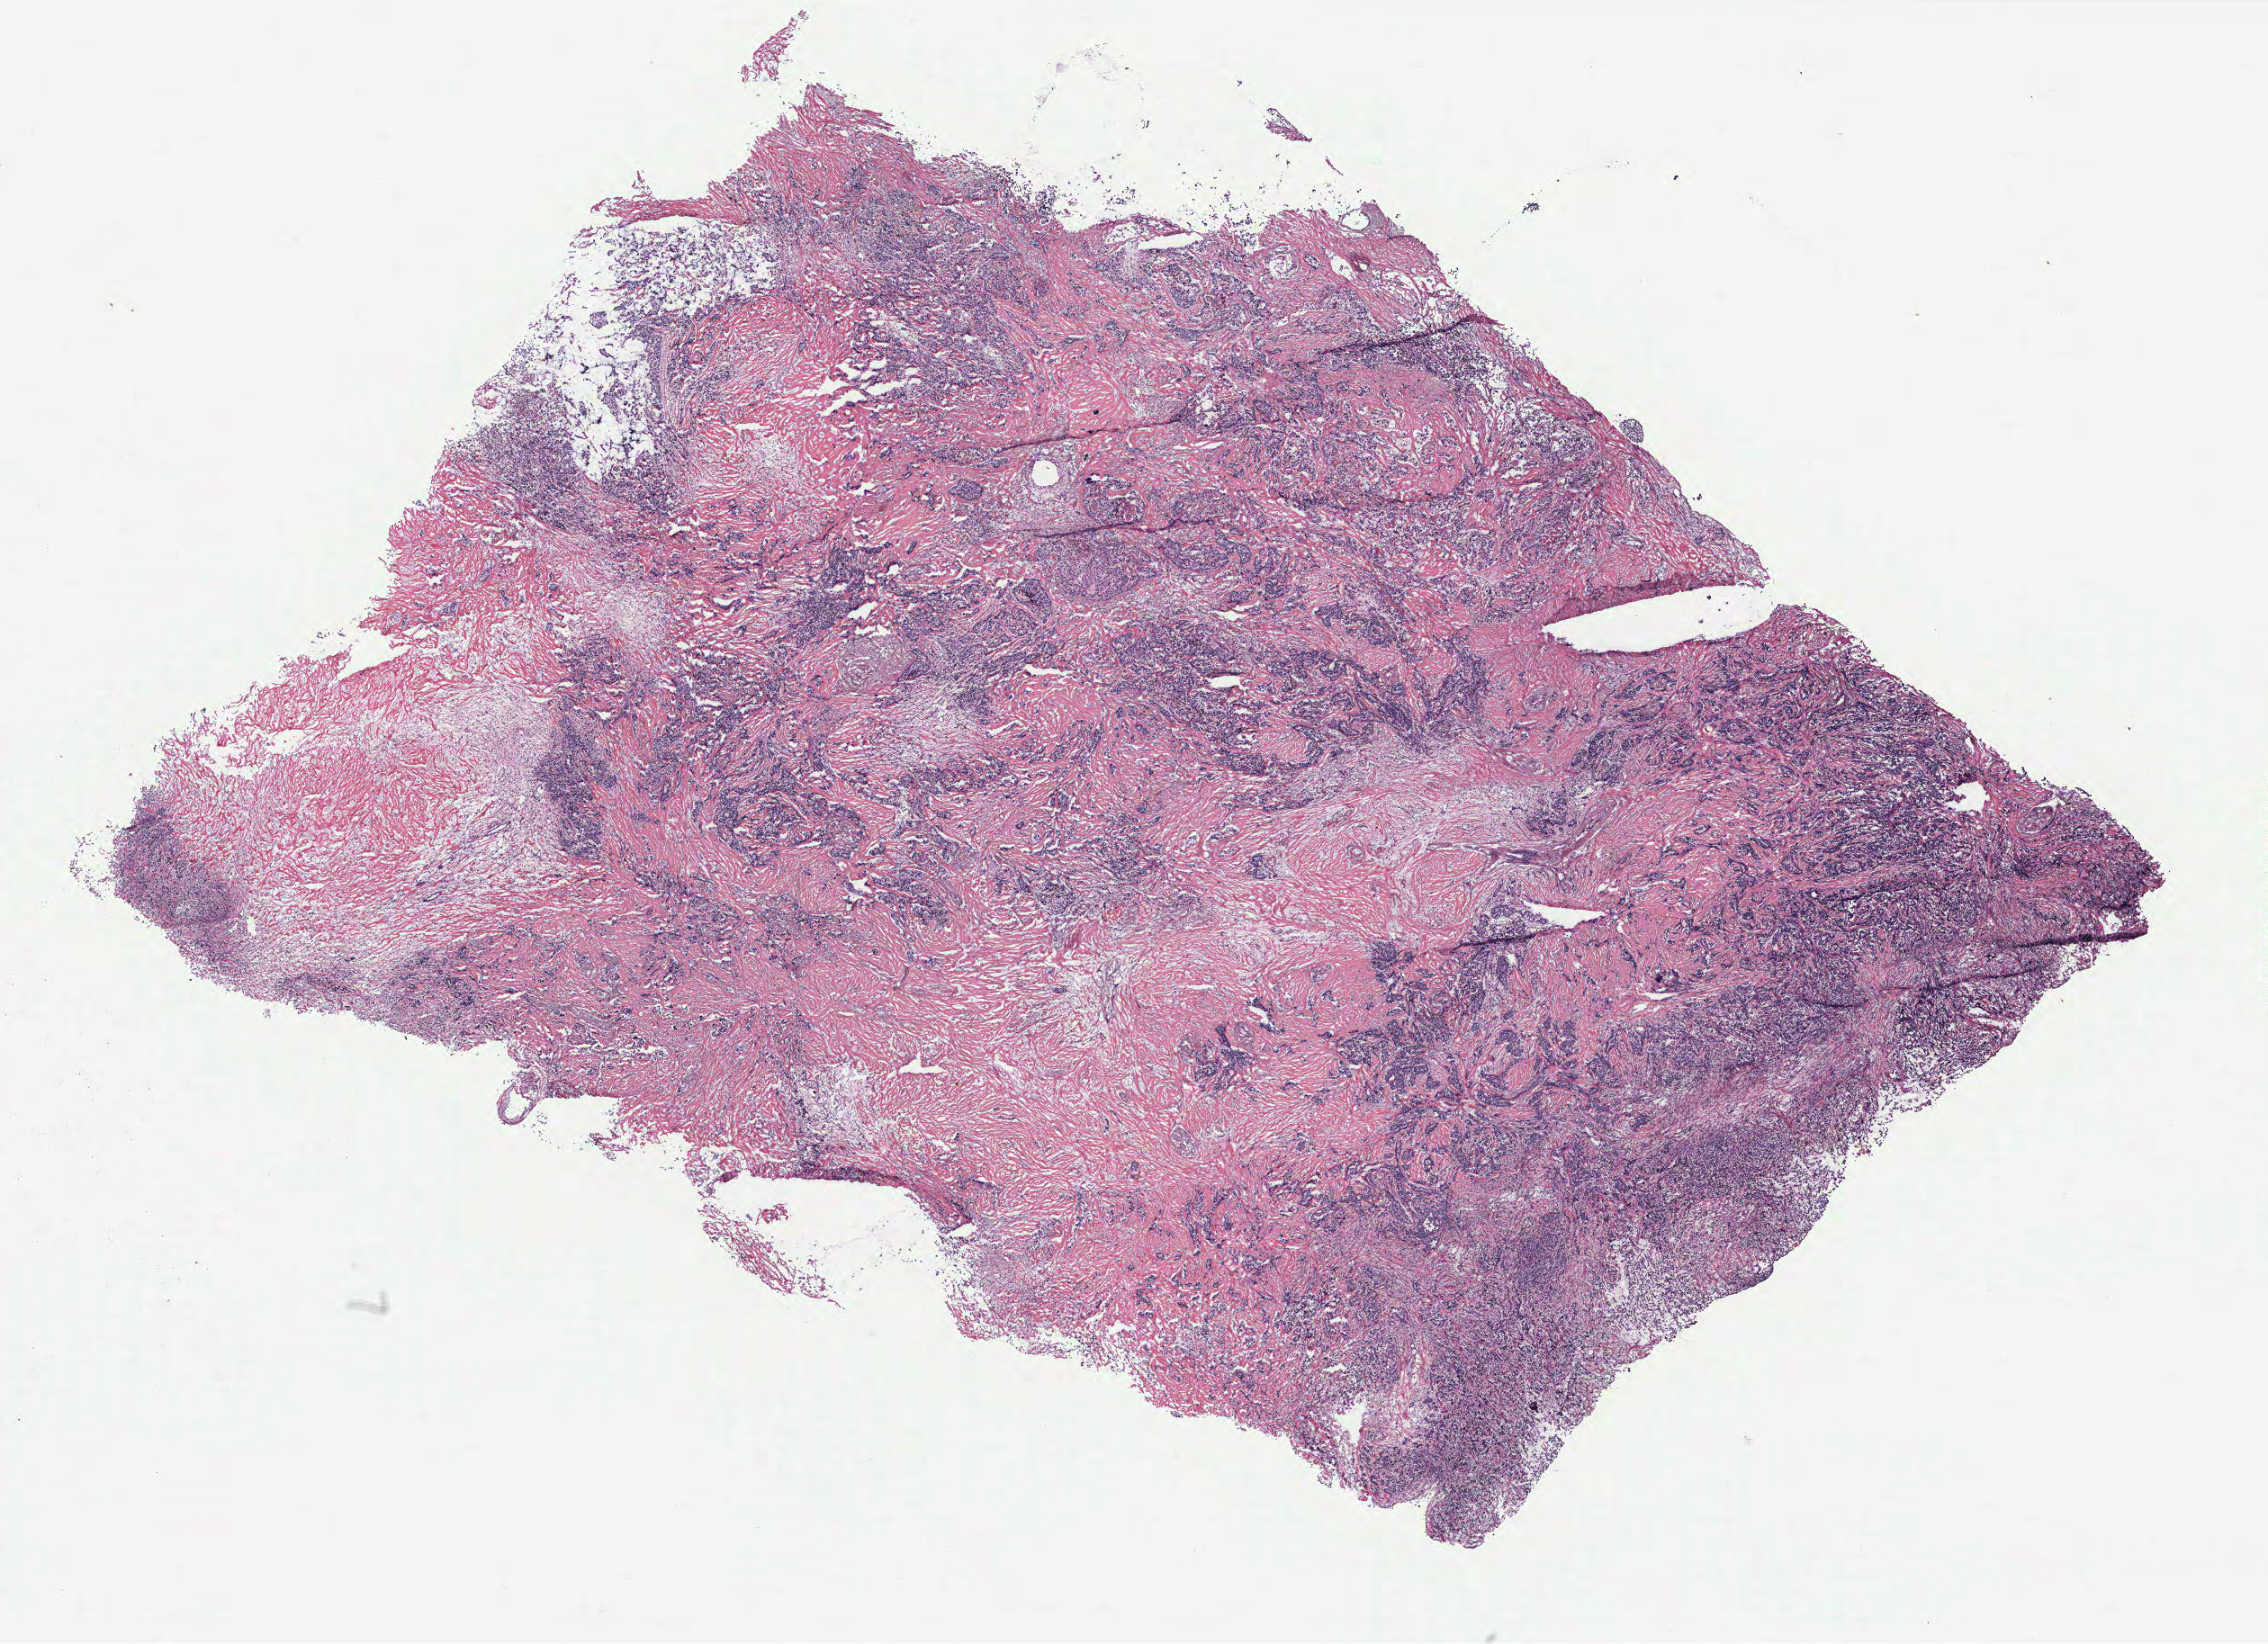
H&E whole-slide image — low-resolution overview of the scanned area, about 20.2 x 14.6 mm (acquisition: 40x scan), breast, tumour tissue. Female, 65 y/o.
* diagnosis: Infiltrating duct carcinoma, NOS
* AJCC pathologic stage: IIIA